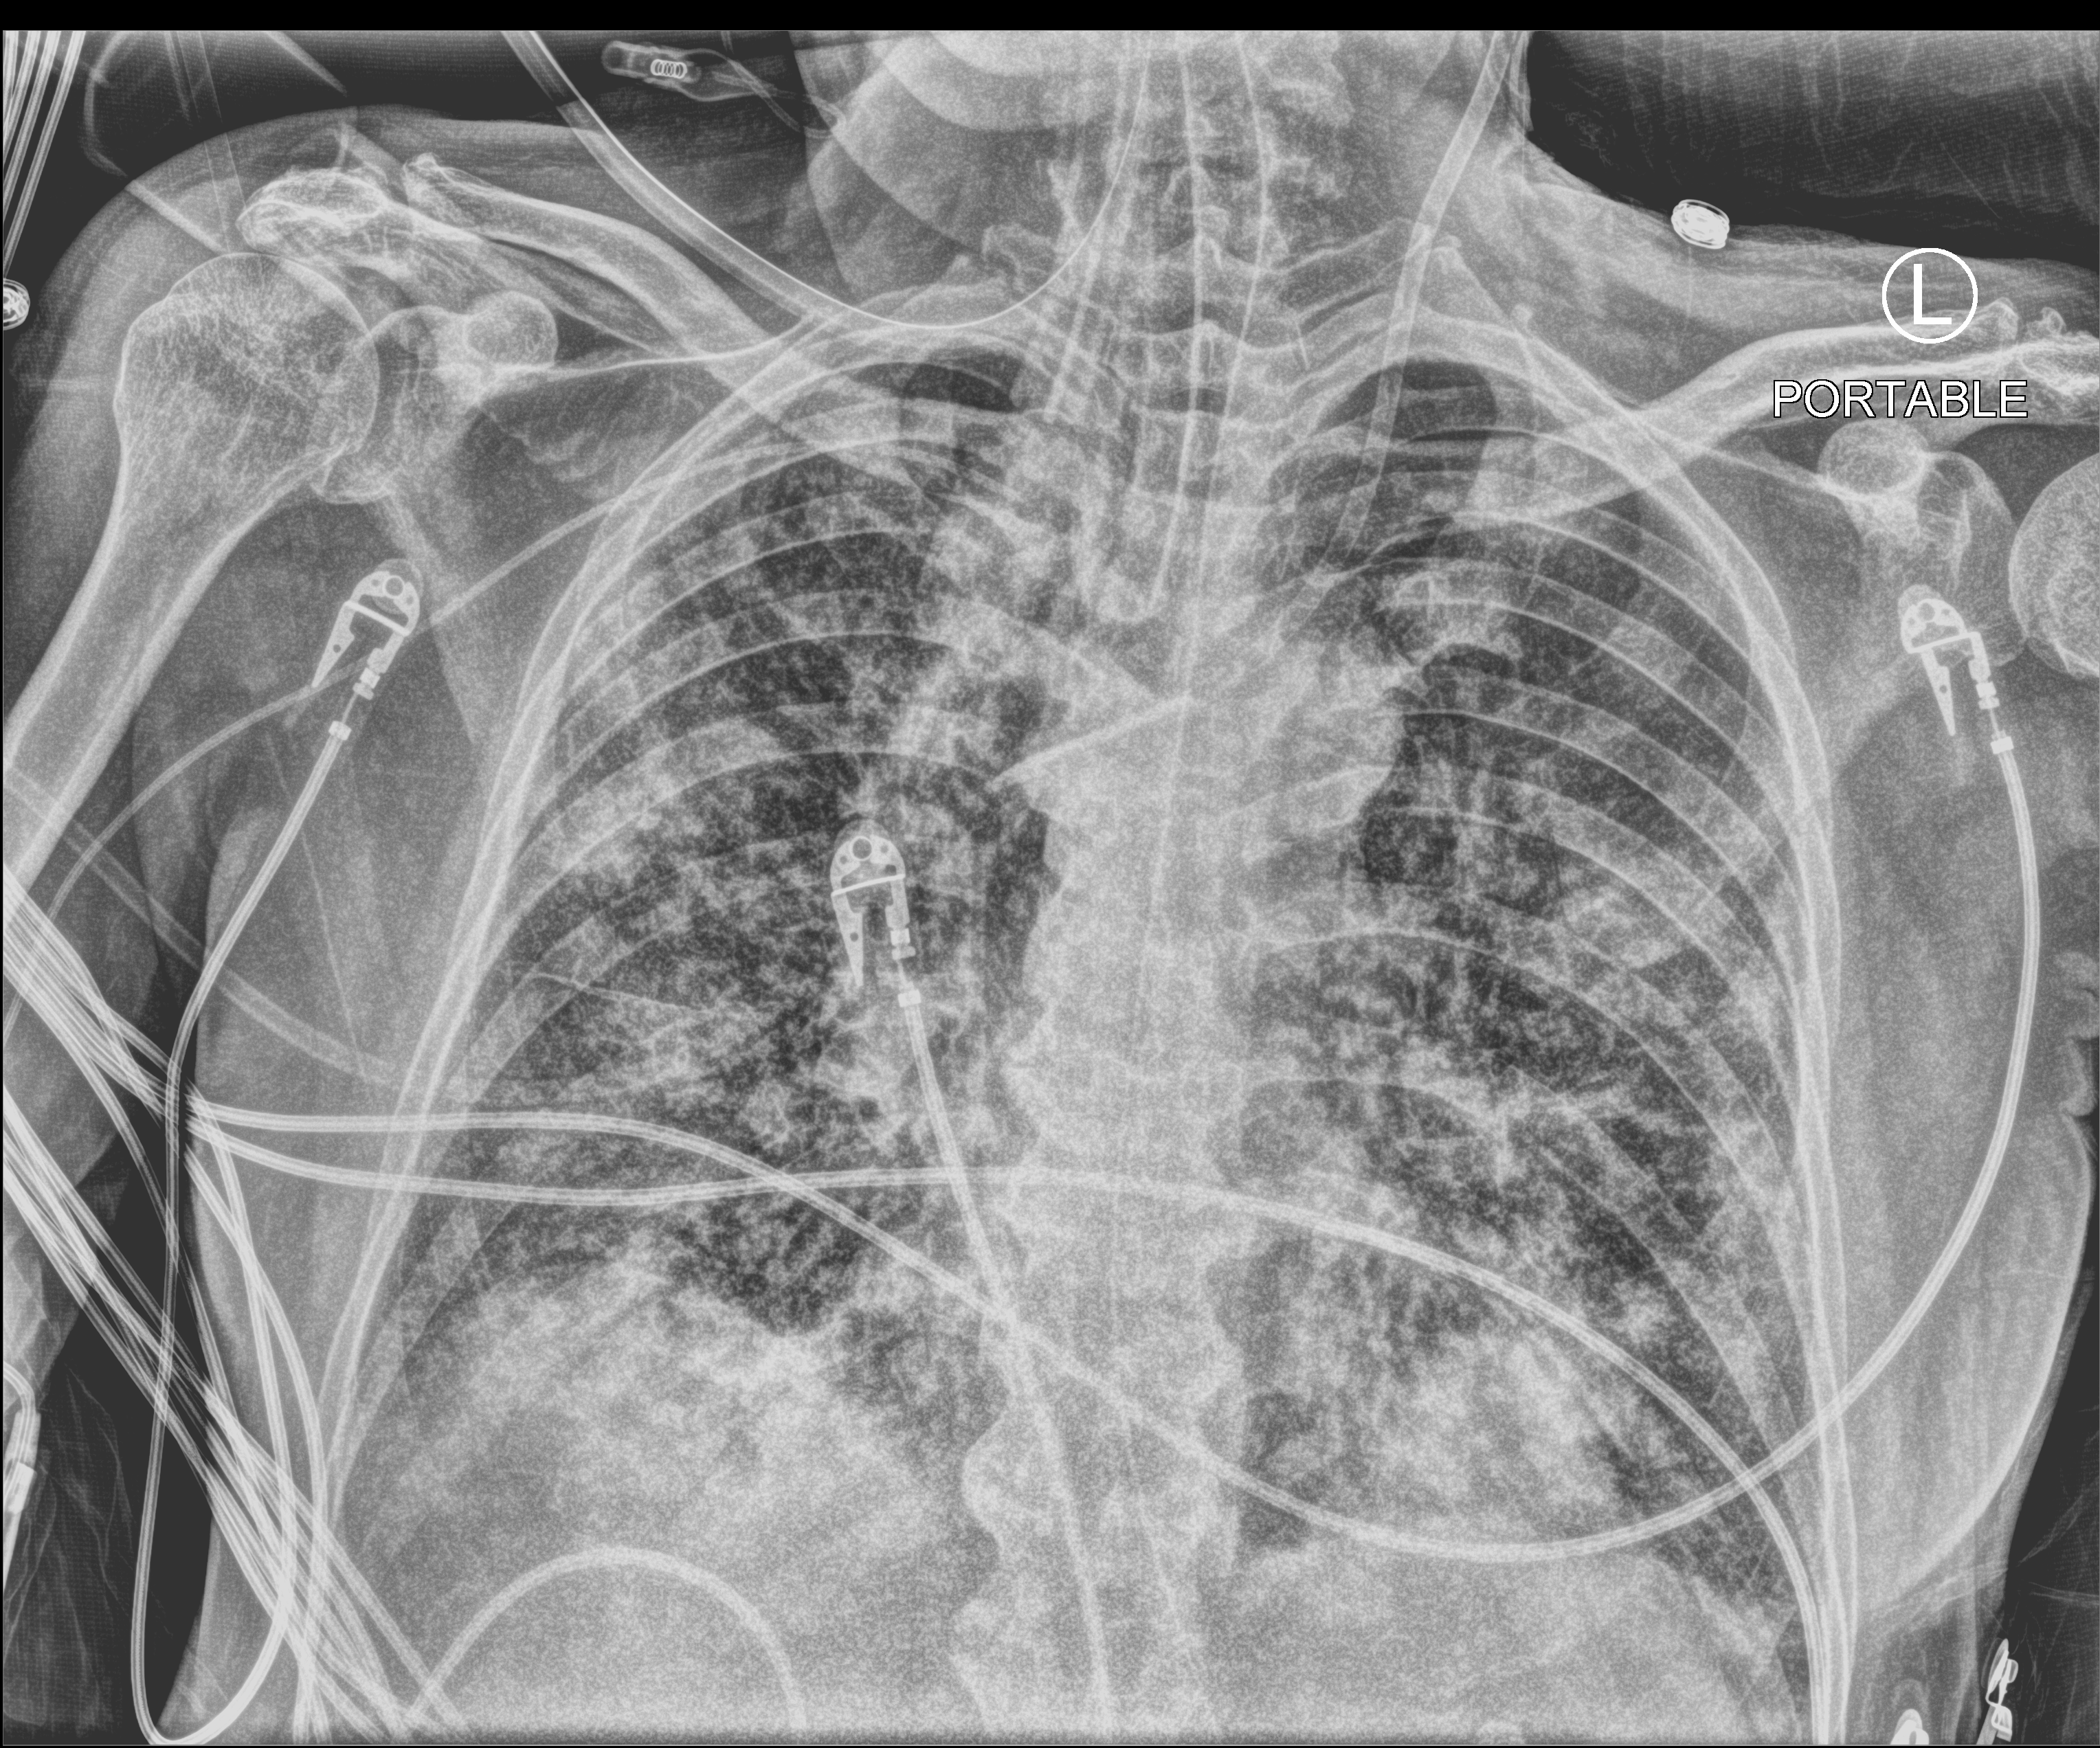
Portable chest radiograph; anteroposterior (AP) projection. Patient hospitalised with COVID-19; male, aged 60–74 years.
Admission-level facts for this patient (not findings on this image; timing relative to this image not recorded):
- admitted to intensive care during this hospital stay: yes
- other chronic lung disease (admission record): no